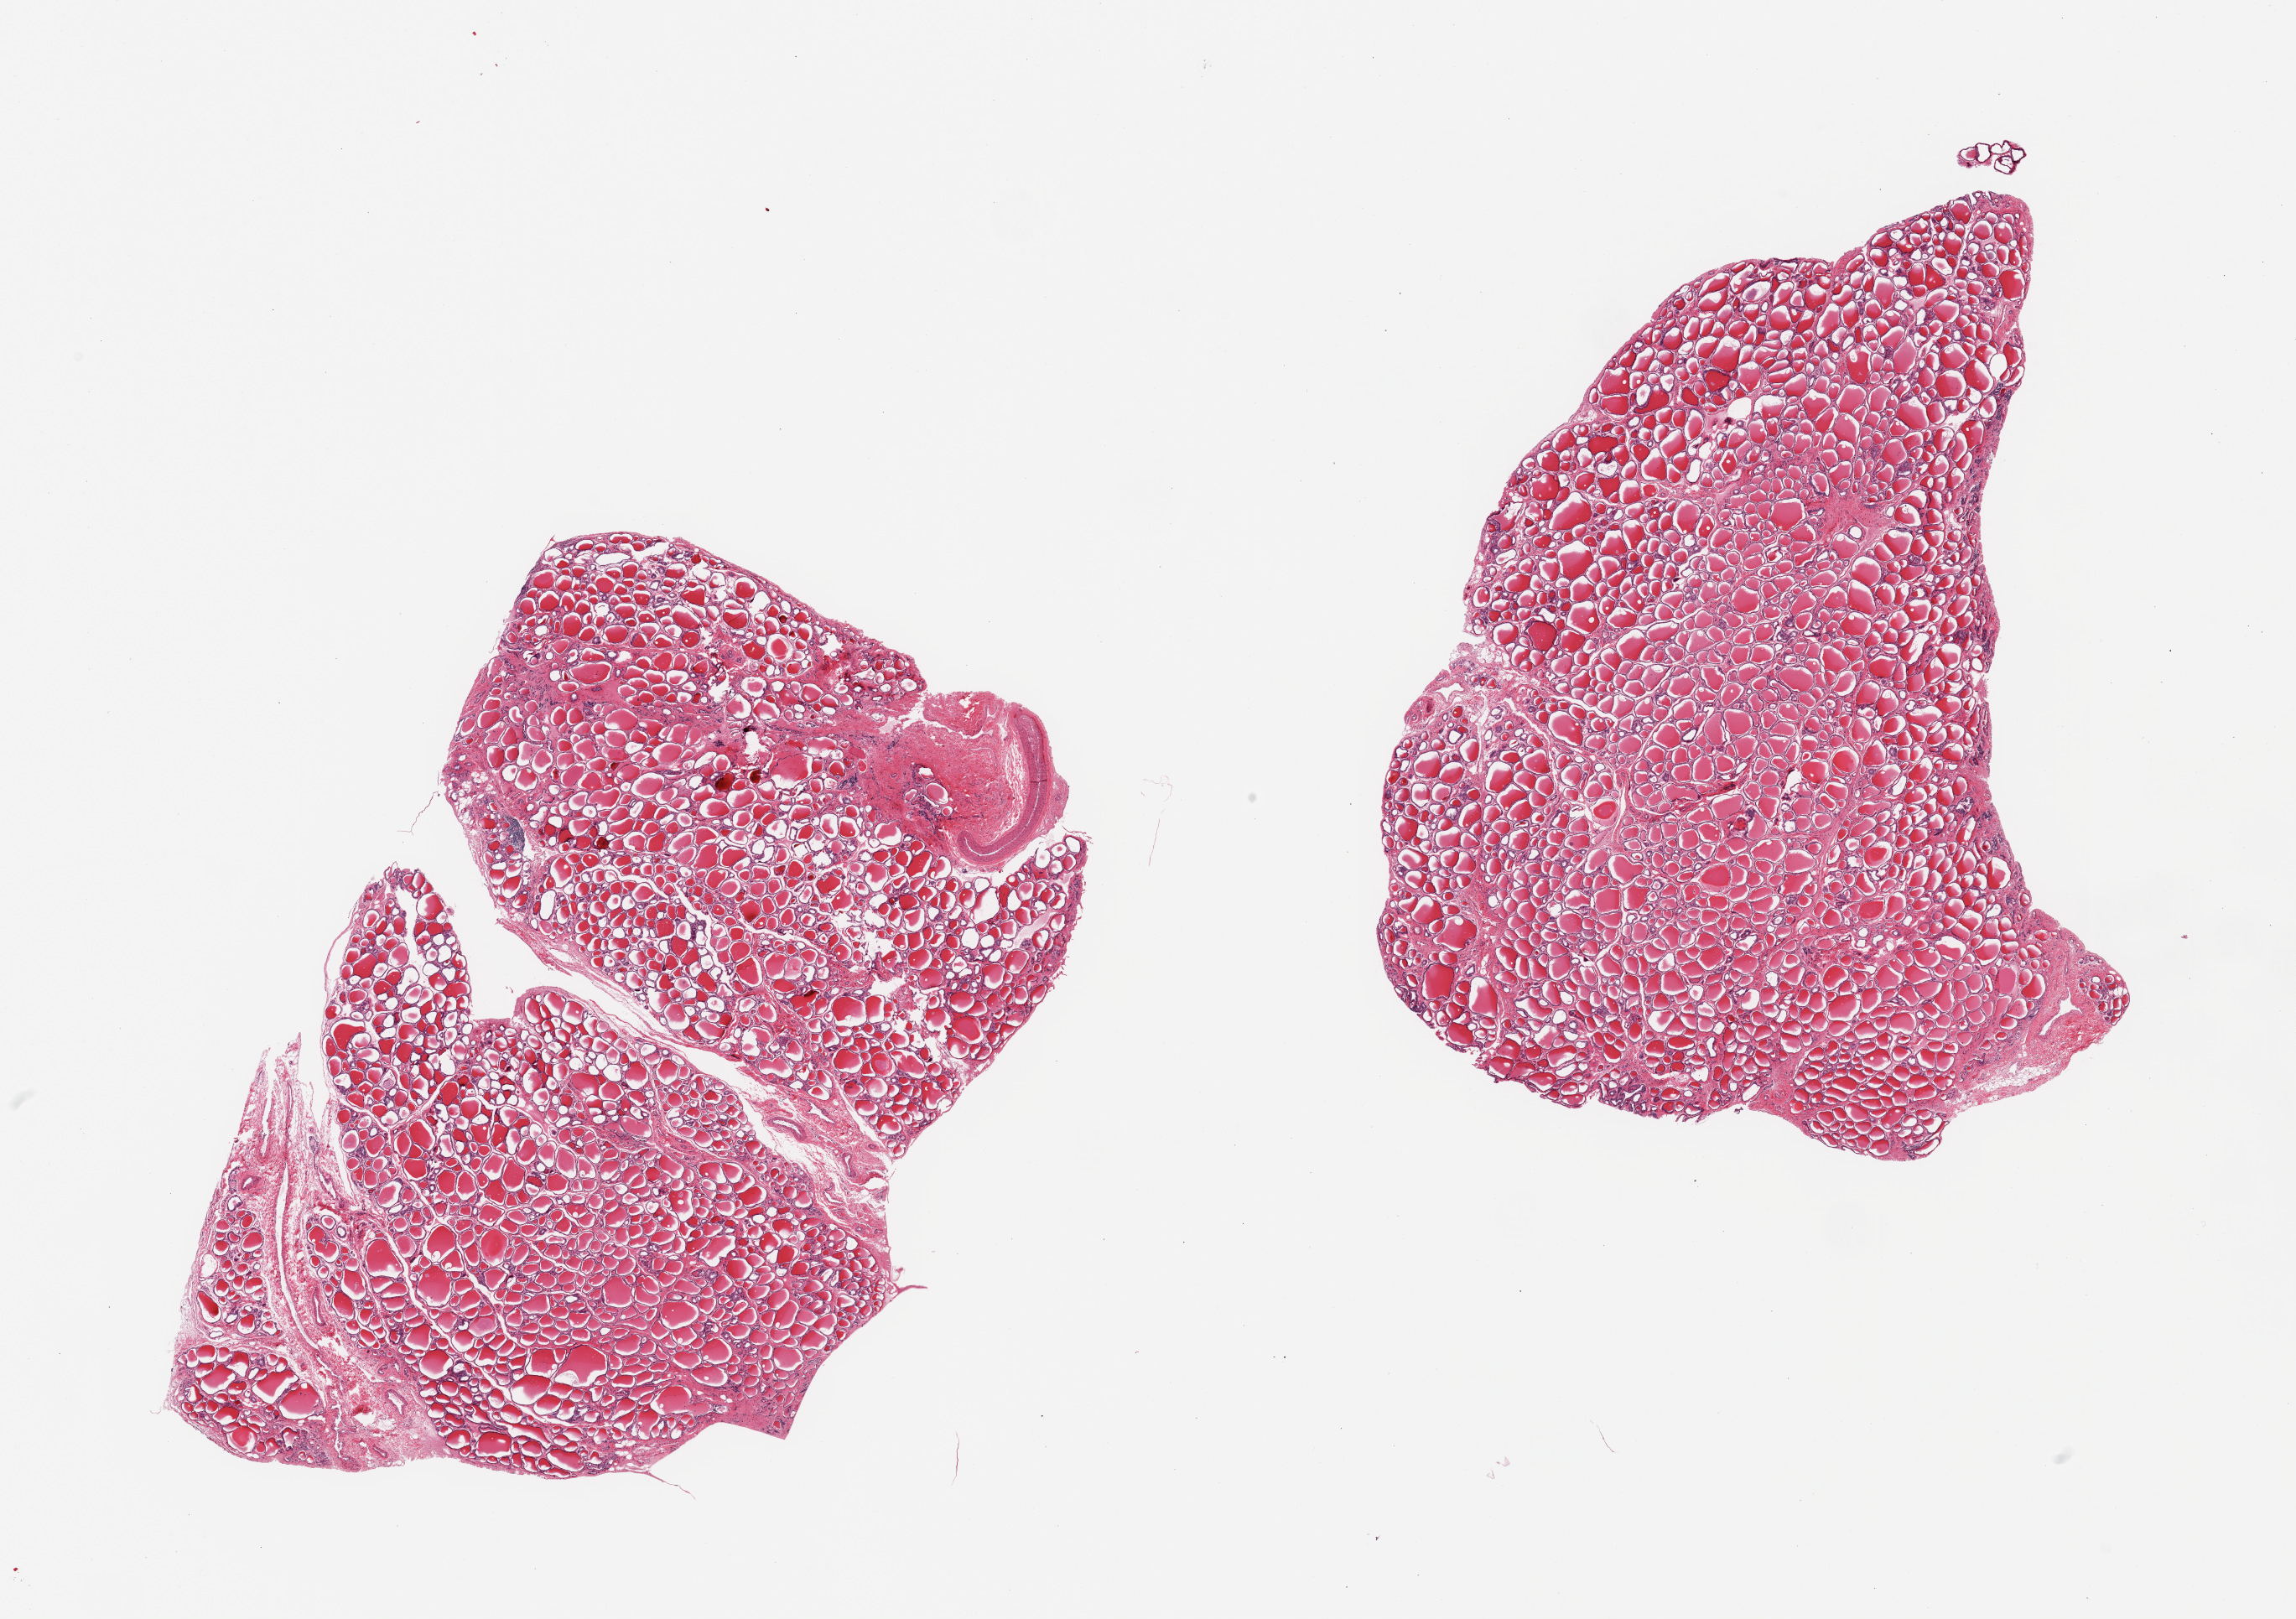
Whole-slide image, hematoxylin and eosin (H&E) stain, low-resolution overview of the scanned area, about 21.7 x 15.3 mm; PAXgene-fixed paraffin-embedded (PFPE) section; section of thyroid (target tissue); donor tissue sample. Female donor.
* pathologist's review note for this sample: 2 pieces; 1.7 mm fibrovascular focus at edge of 1 piece